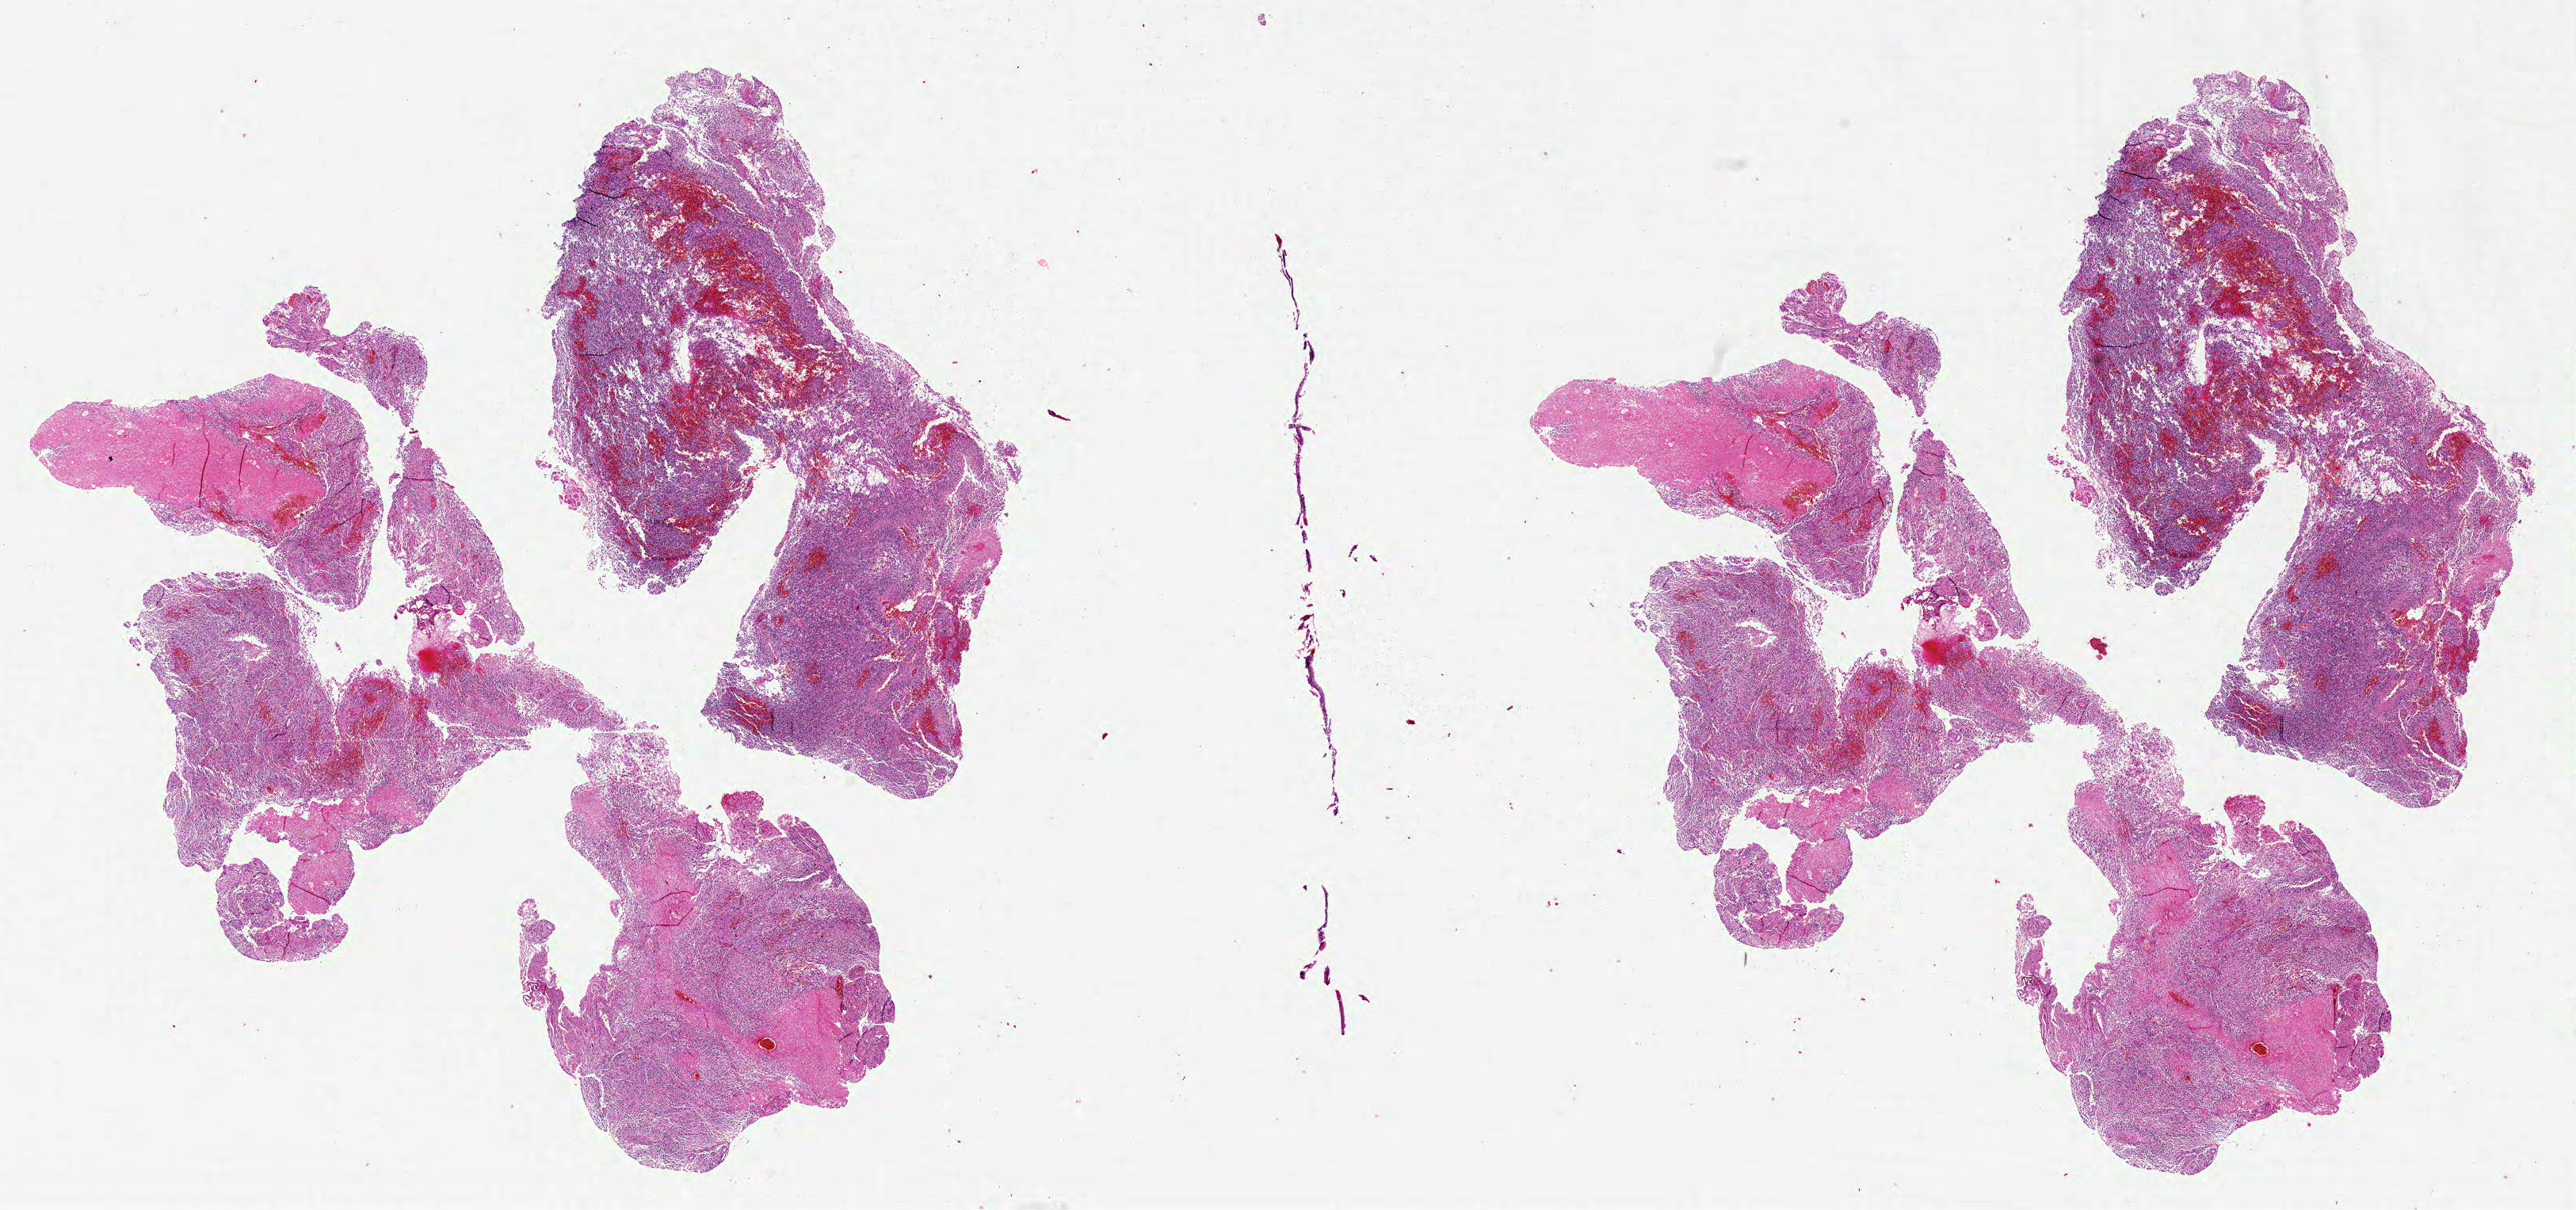
H&E whole-slide image — whole scanned area (about 26.0 x 12.2 mm, slide scanned at 20x) shown as a low-resolution overview; formalin-fixed paraffin-embedded (FFPE) diagnostic section; sample: primary tumour, brain. Male patient; age at initial diagnosis 52 years.
Histologic diagnosis: Glioblastoma.